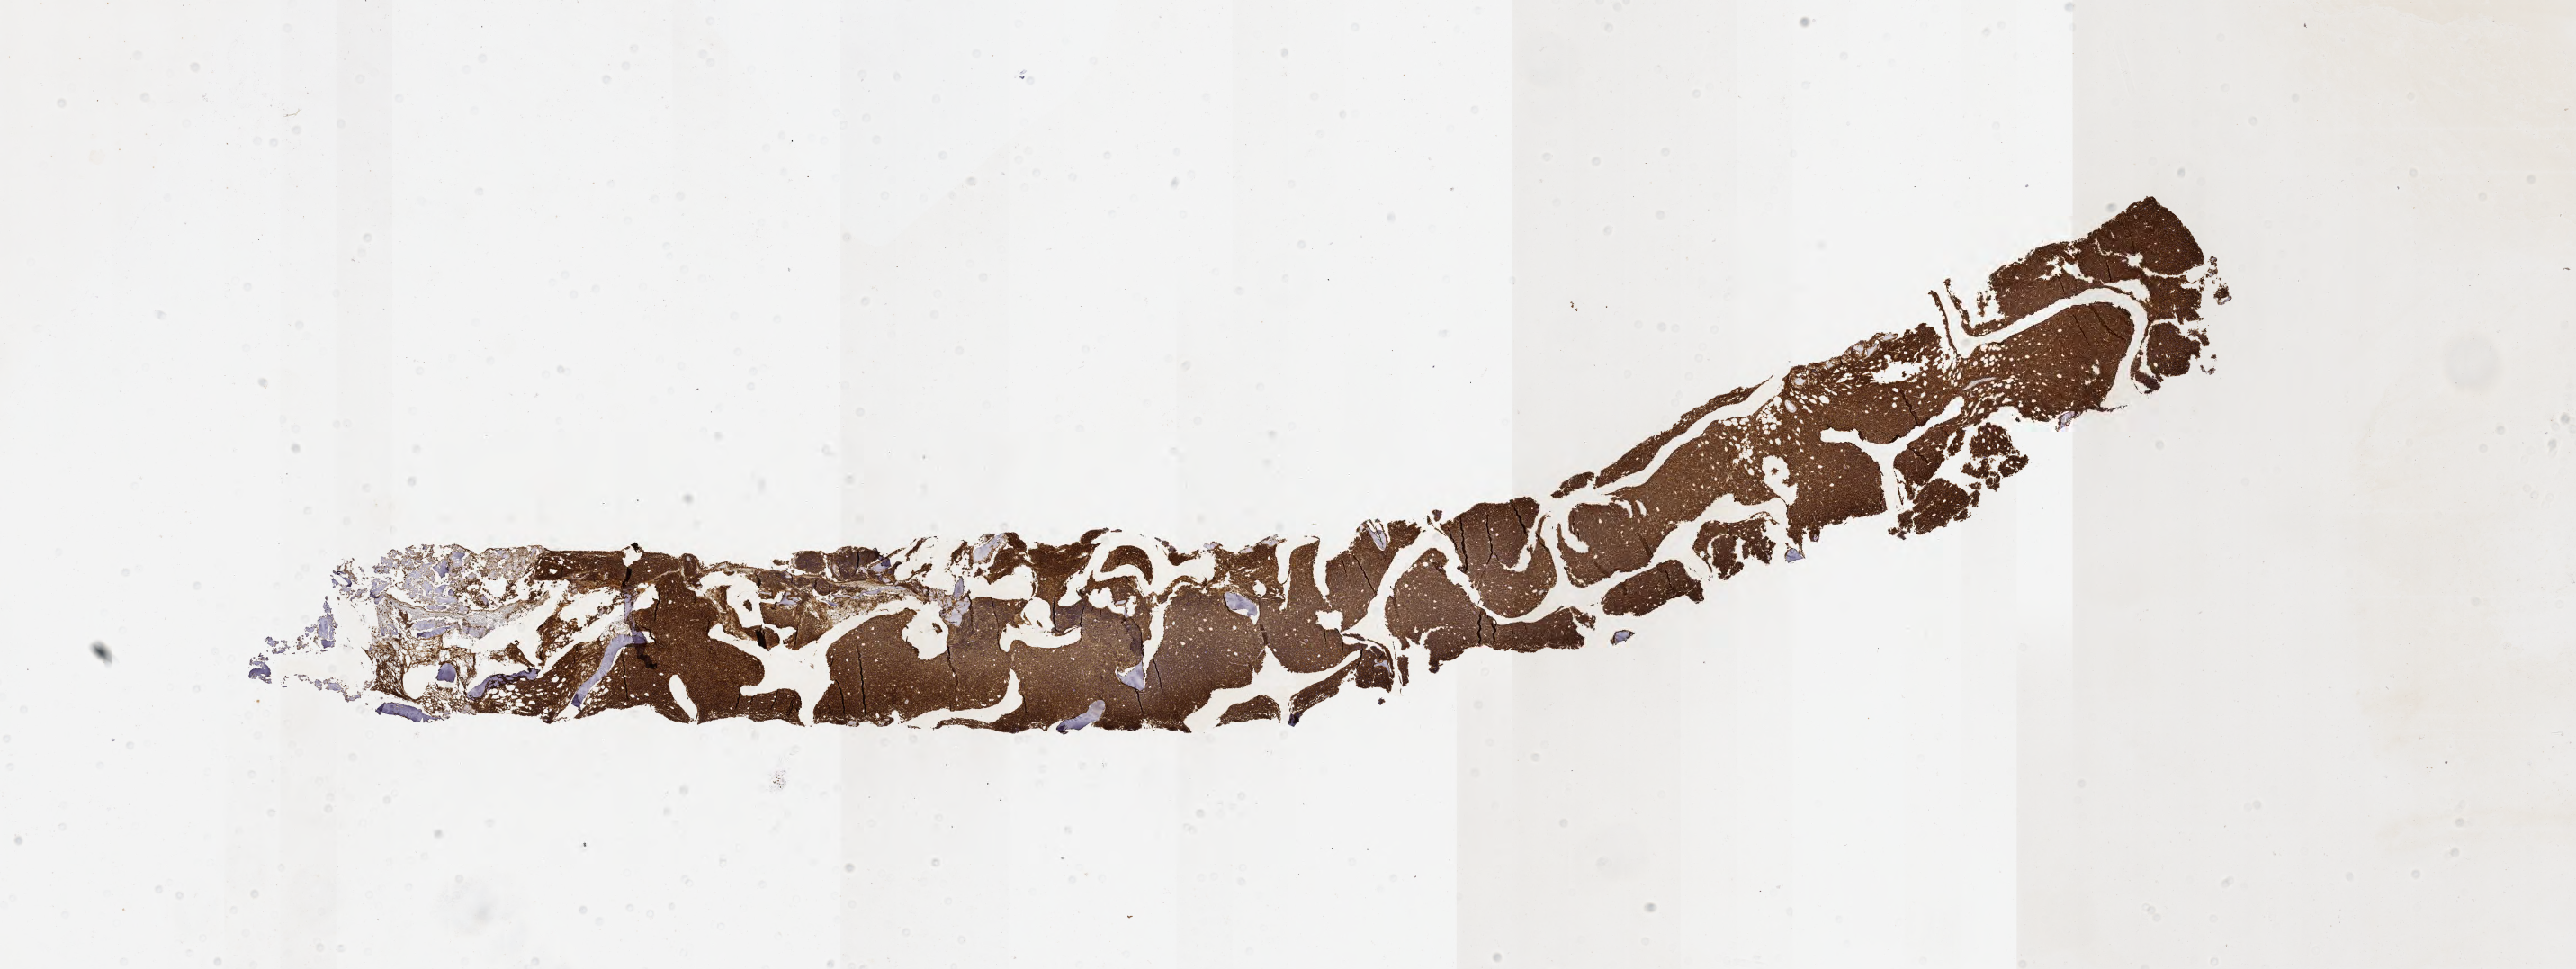
Whole-slide image, immunohistochemical stain for CD10 — a low-resolution overview of the entire scanned area, about 23.1 x 8.7 mm, tumor tissue. Patient sex: male.
Diagnosis: Burkitt lymphoma, NOS.